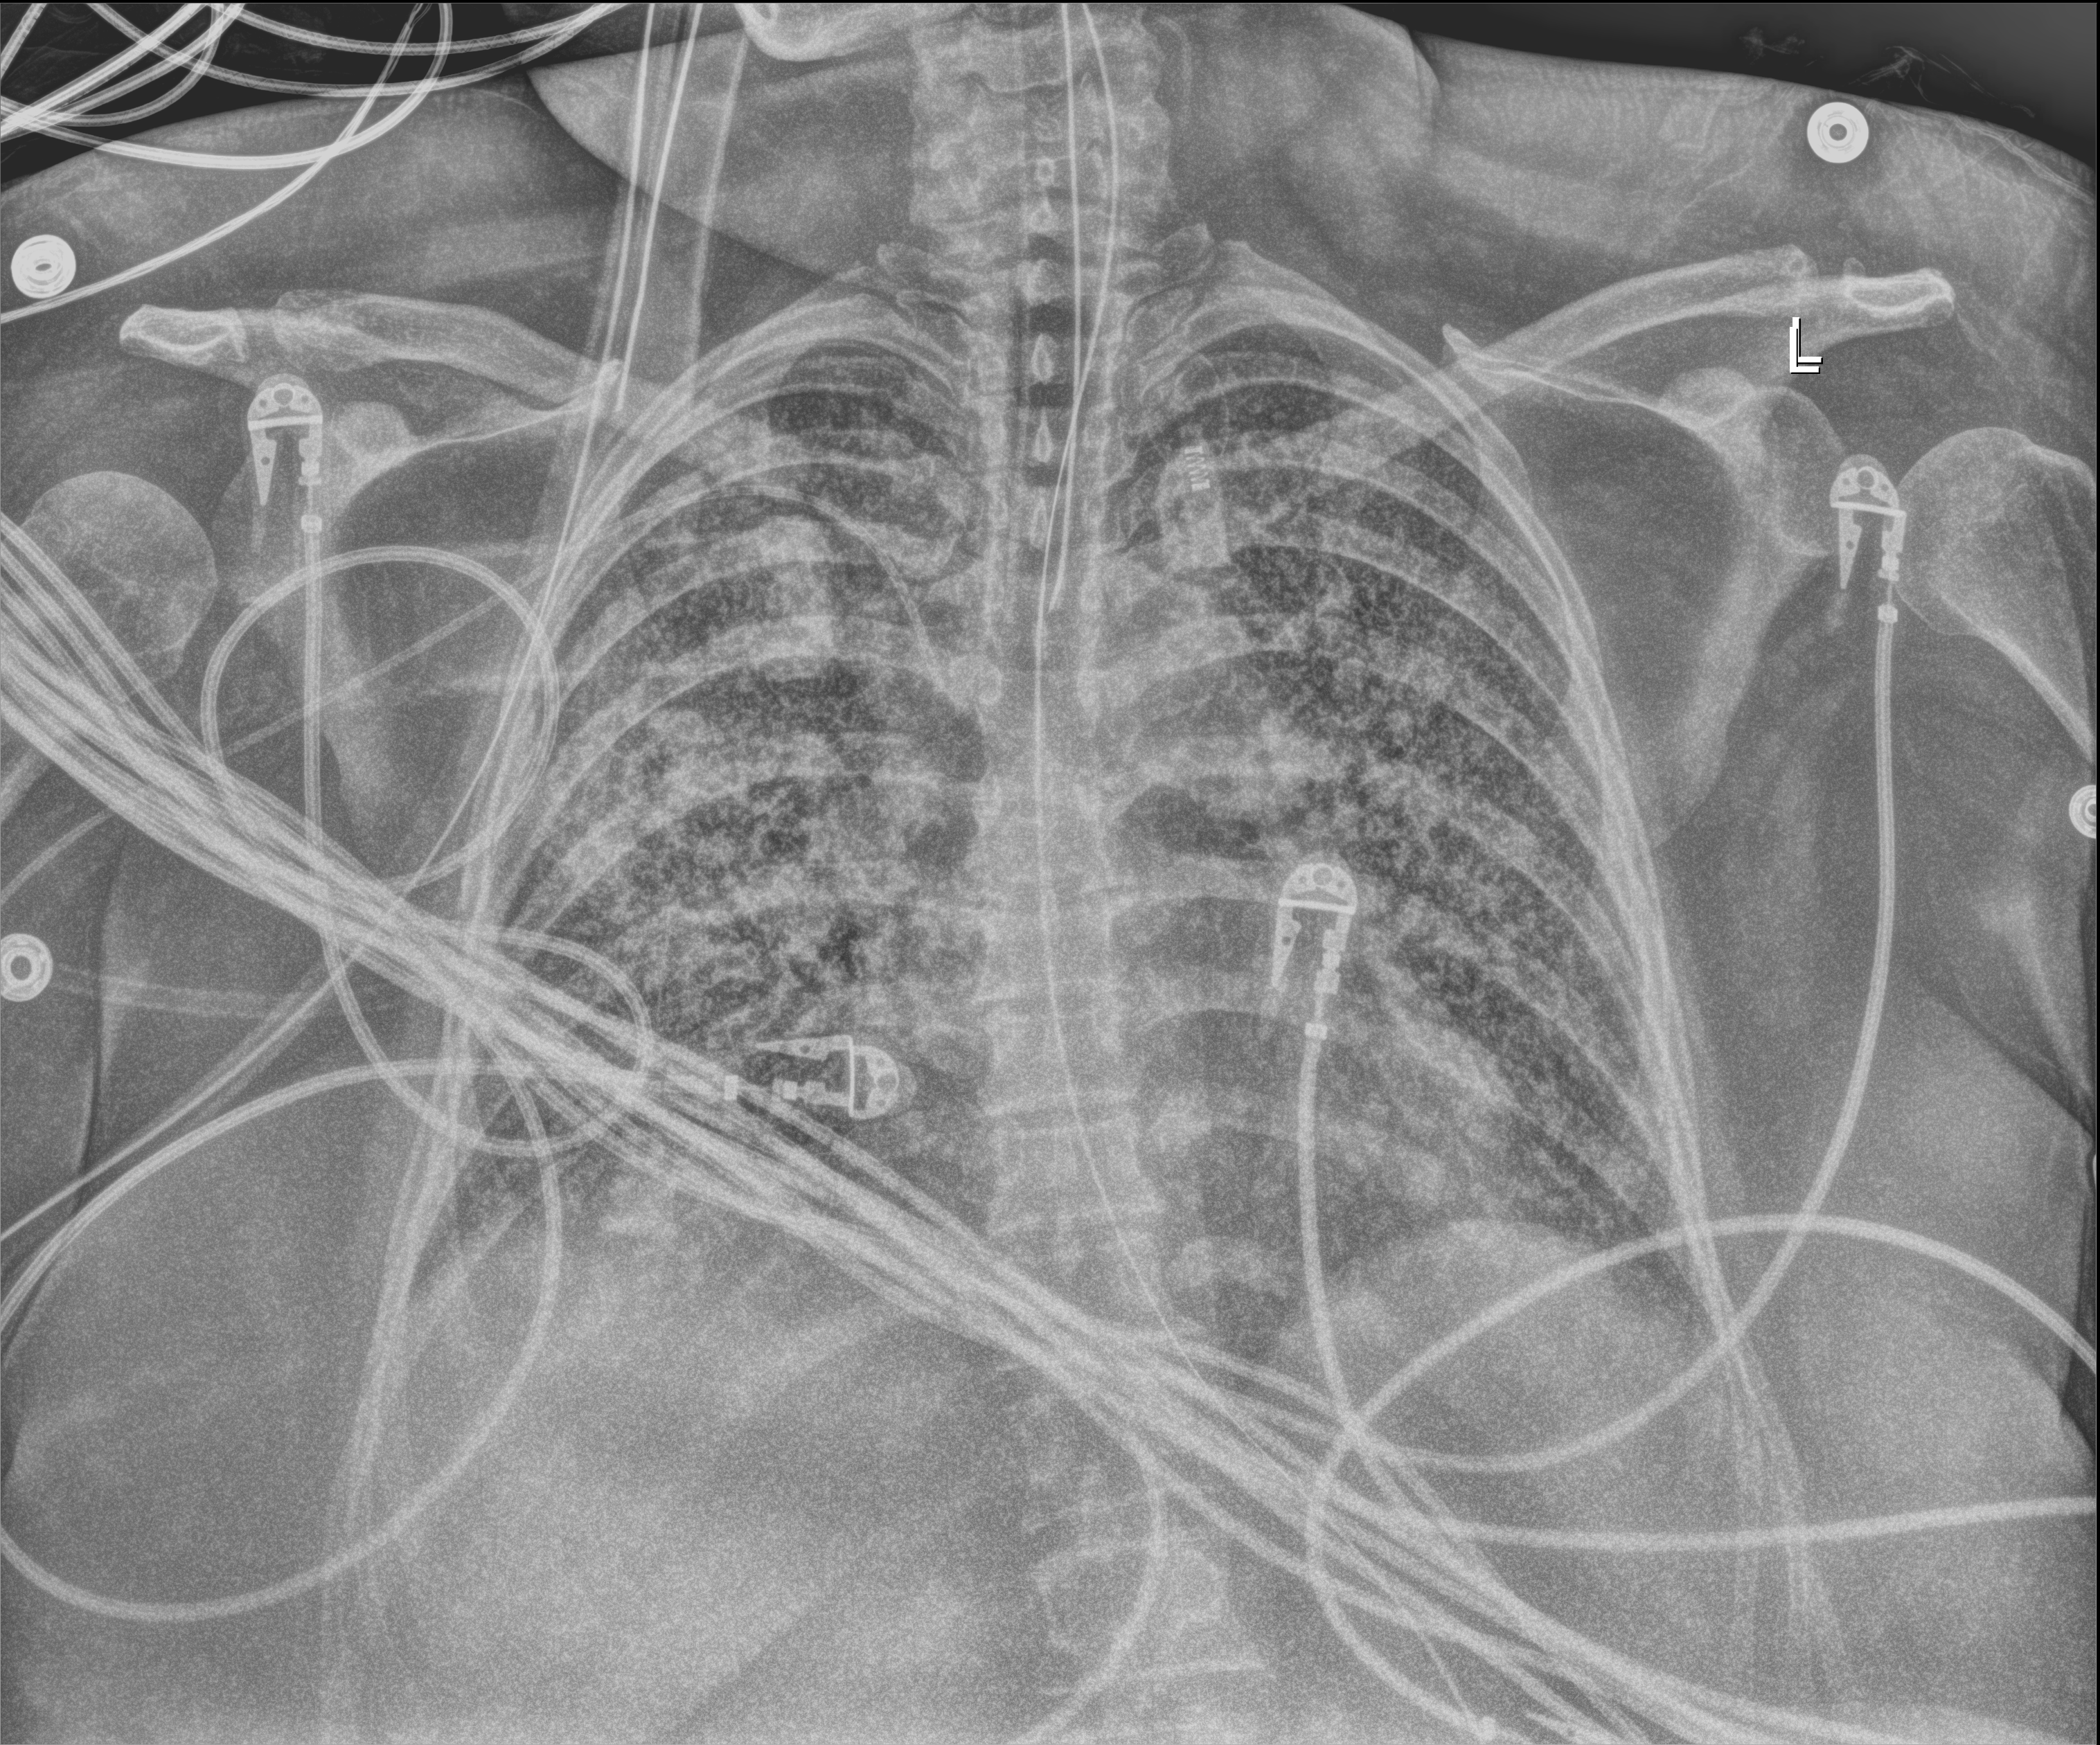
Chest X-ray (portable); anteroposterior (AP) projection. Patient hospitalised with COVID-19; female, aged 18–59 years.
Admission-level facts for this patient (not findings on this image; timing relative to this image not recorded): admitted to intensive care during this hospital stay: yes.